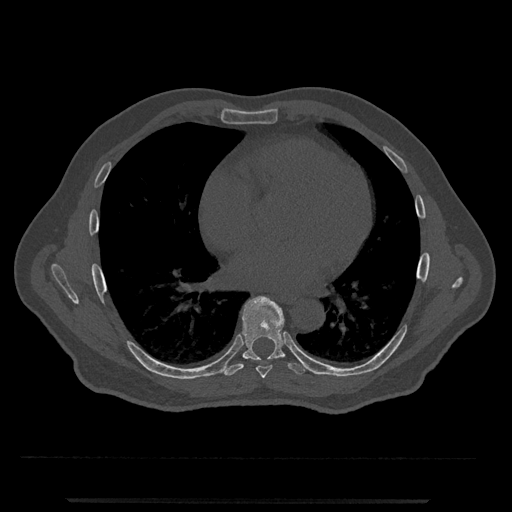
CT including the spine, one axial slice. Position 651 of 797 along the scan axis. Reconstruction kernel Br40s/3. 120 kVp. Bone window (W 1800 / L 400 HU). 0.5 mm slice thickness. 512 × 512 image matrix, field of view 419 × 419 mm. Male patient, age 63 years. From the clinical record (not read from this slice): primary cancer: prostate.
Annotated regions visible in this slice (semi-automatically segmented with operator editing):
- T7 vertebra: box from (x=256, y=365) to (x=272, y=379) px
- T8 vertebra: (x=224, y=296)–(x=306, y=376)